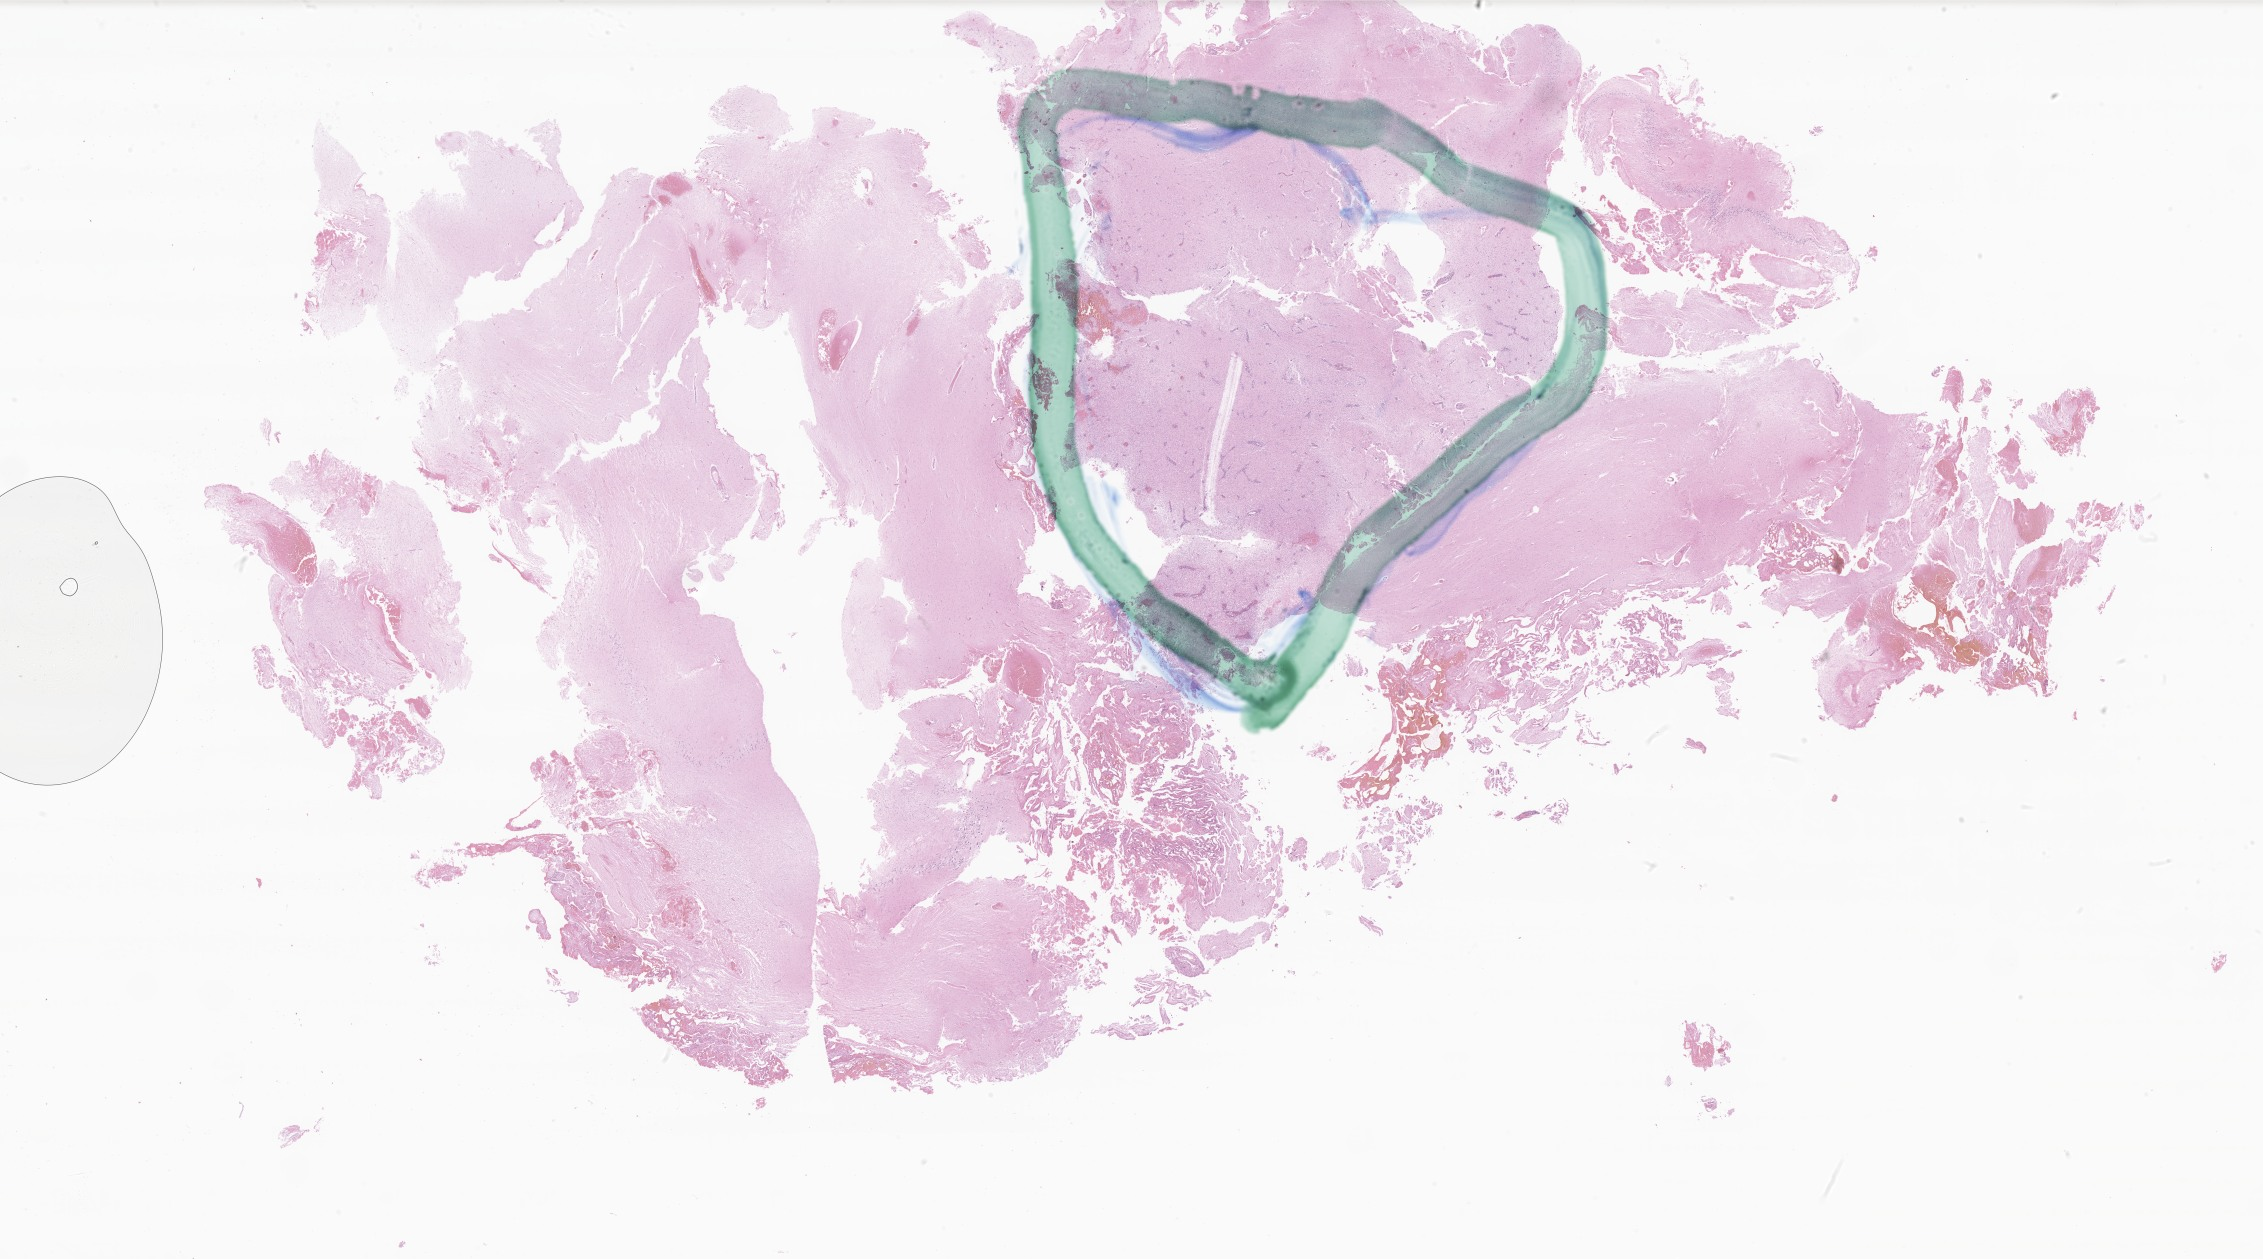
Whole-slide image, H&E stain of tumor tissue from the cerebellum, whole scanned area (about 38.2 x 21.2 mm) shown as a low-resolution overview, formalin-fixed, paraffin-embedded (FFPE) tissue. Male patient, age 80 months (6 years 8 months).
- diagnosis: Pilocytic astrocytoma